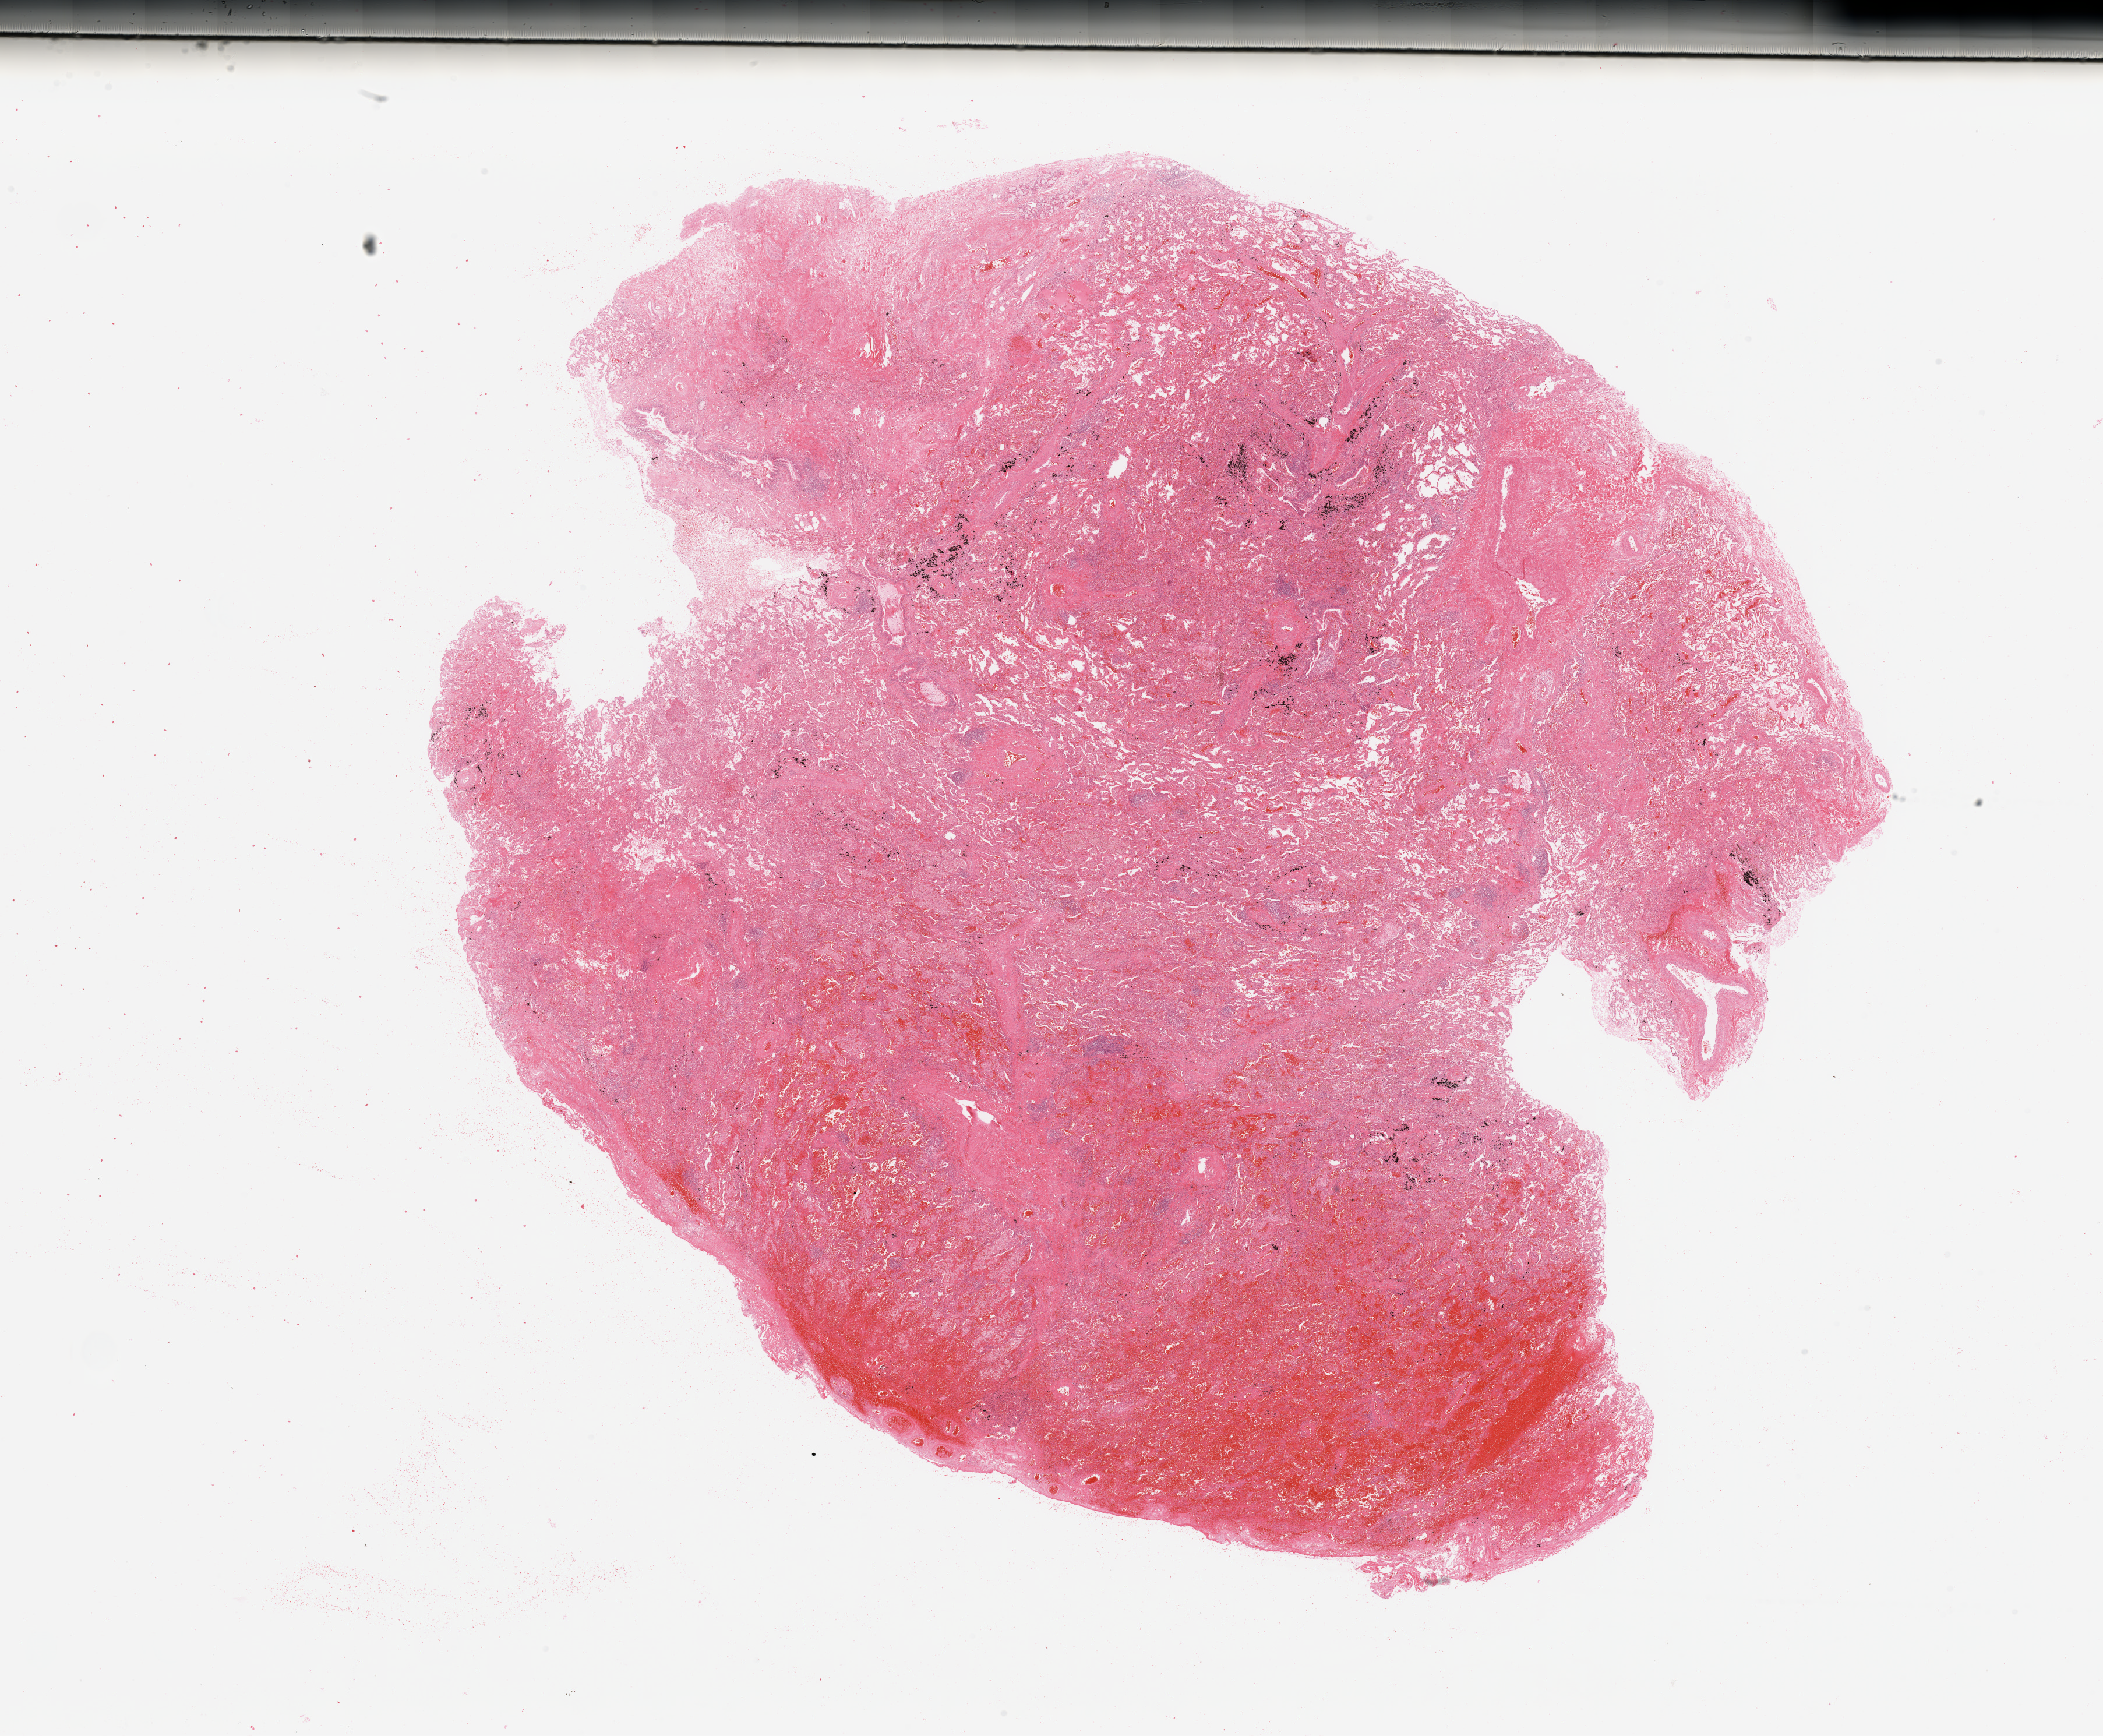
Whole-slide histology image, Hematoxylin and eosin (H&E) stained, whole scanned area (about 28.5 x 23.6 mm) shown as a low-resolution overview. Tumour tissue sample, lung. Male, 59 y/o.
Histologic diagnosis: Adenocarcinoma, NOS.